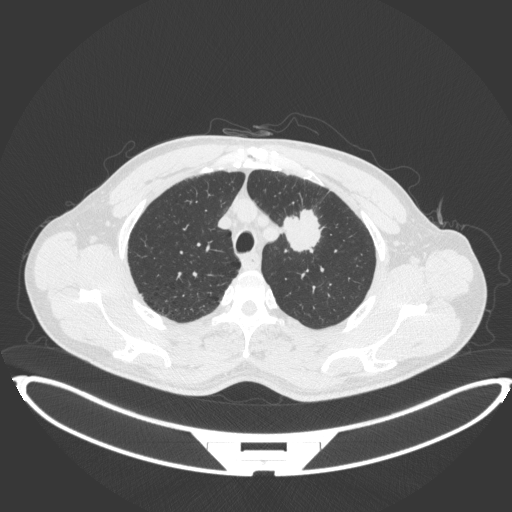
Chest CT, one axial slice; position 351 of 407 along the scan axis; reconstruction kernel B31f; lung window (W 1500 / L -600 HU); 1 mm slice thickness; 512 × 512 image matrix. Patient: male, 60 years. Case-level facts recorded for this patient, not image findings: clinical TNM (as recorded): T2a N0 M0; histopathological grade: G1-G2.
Structures marked on this image (rectangle marked by the reading radiologist):
- lung tumour (recorded histology: squamous cell carcinoma): bounding box <279,208,324,253> (left, top, right, bottom; pixels)